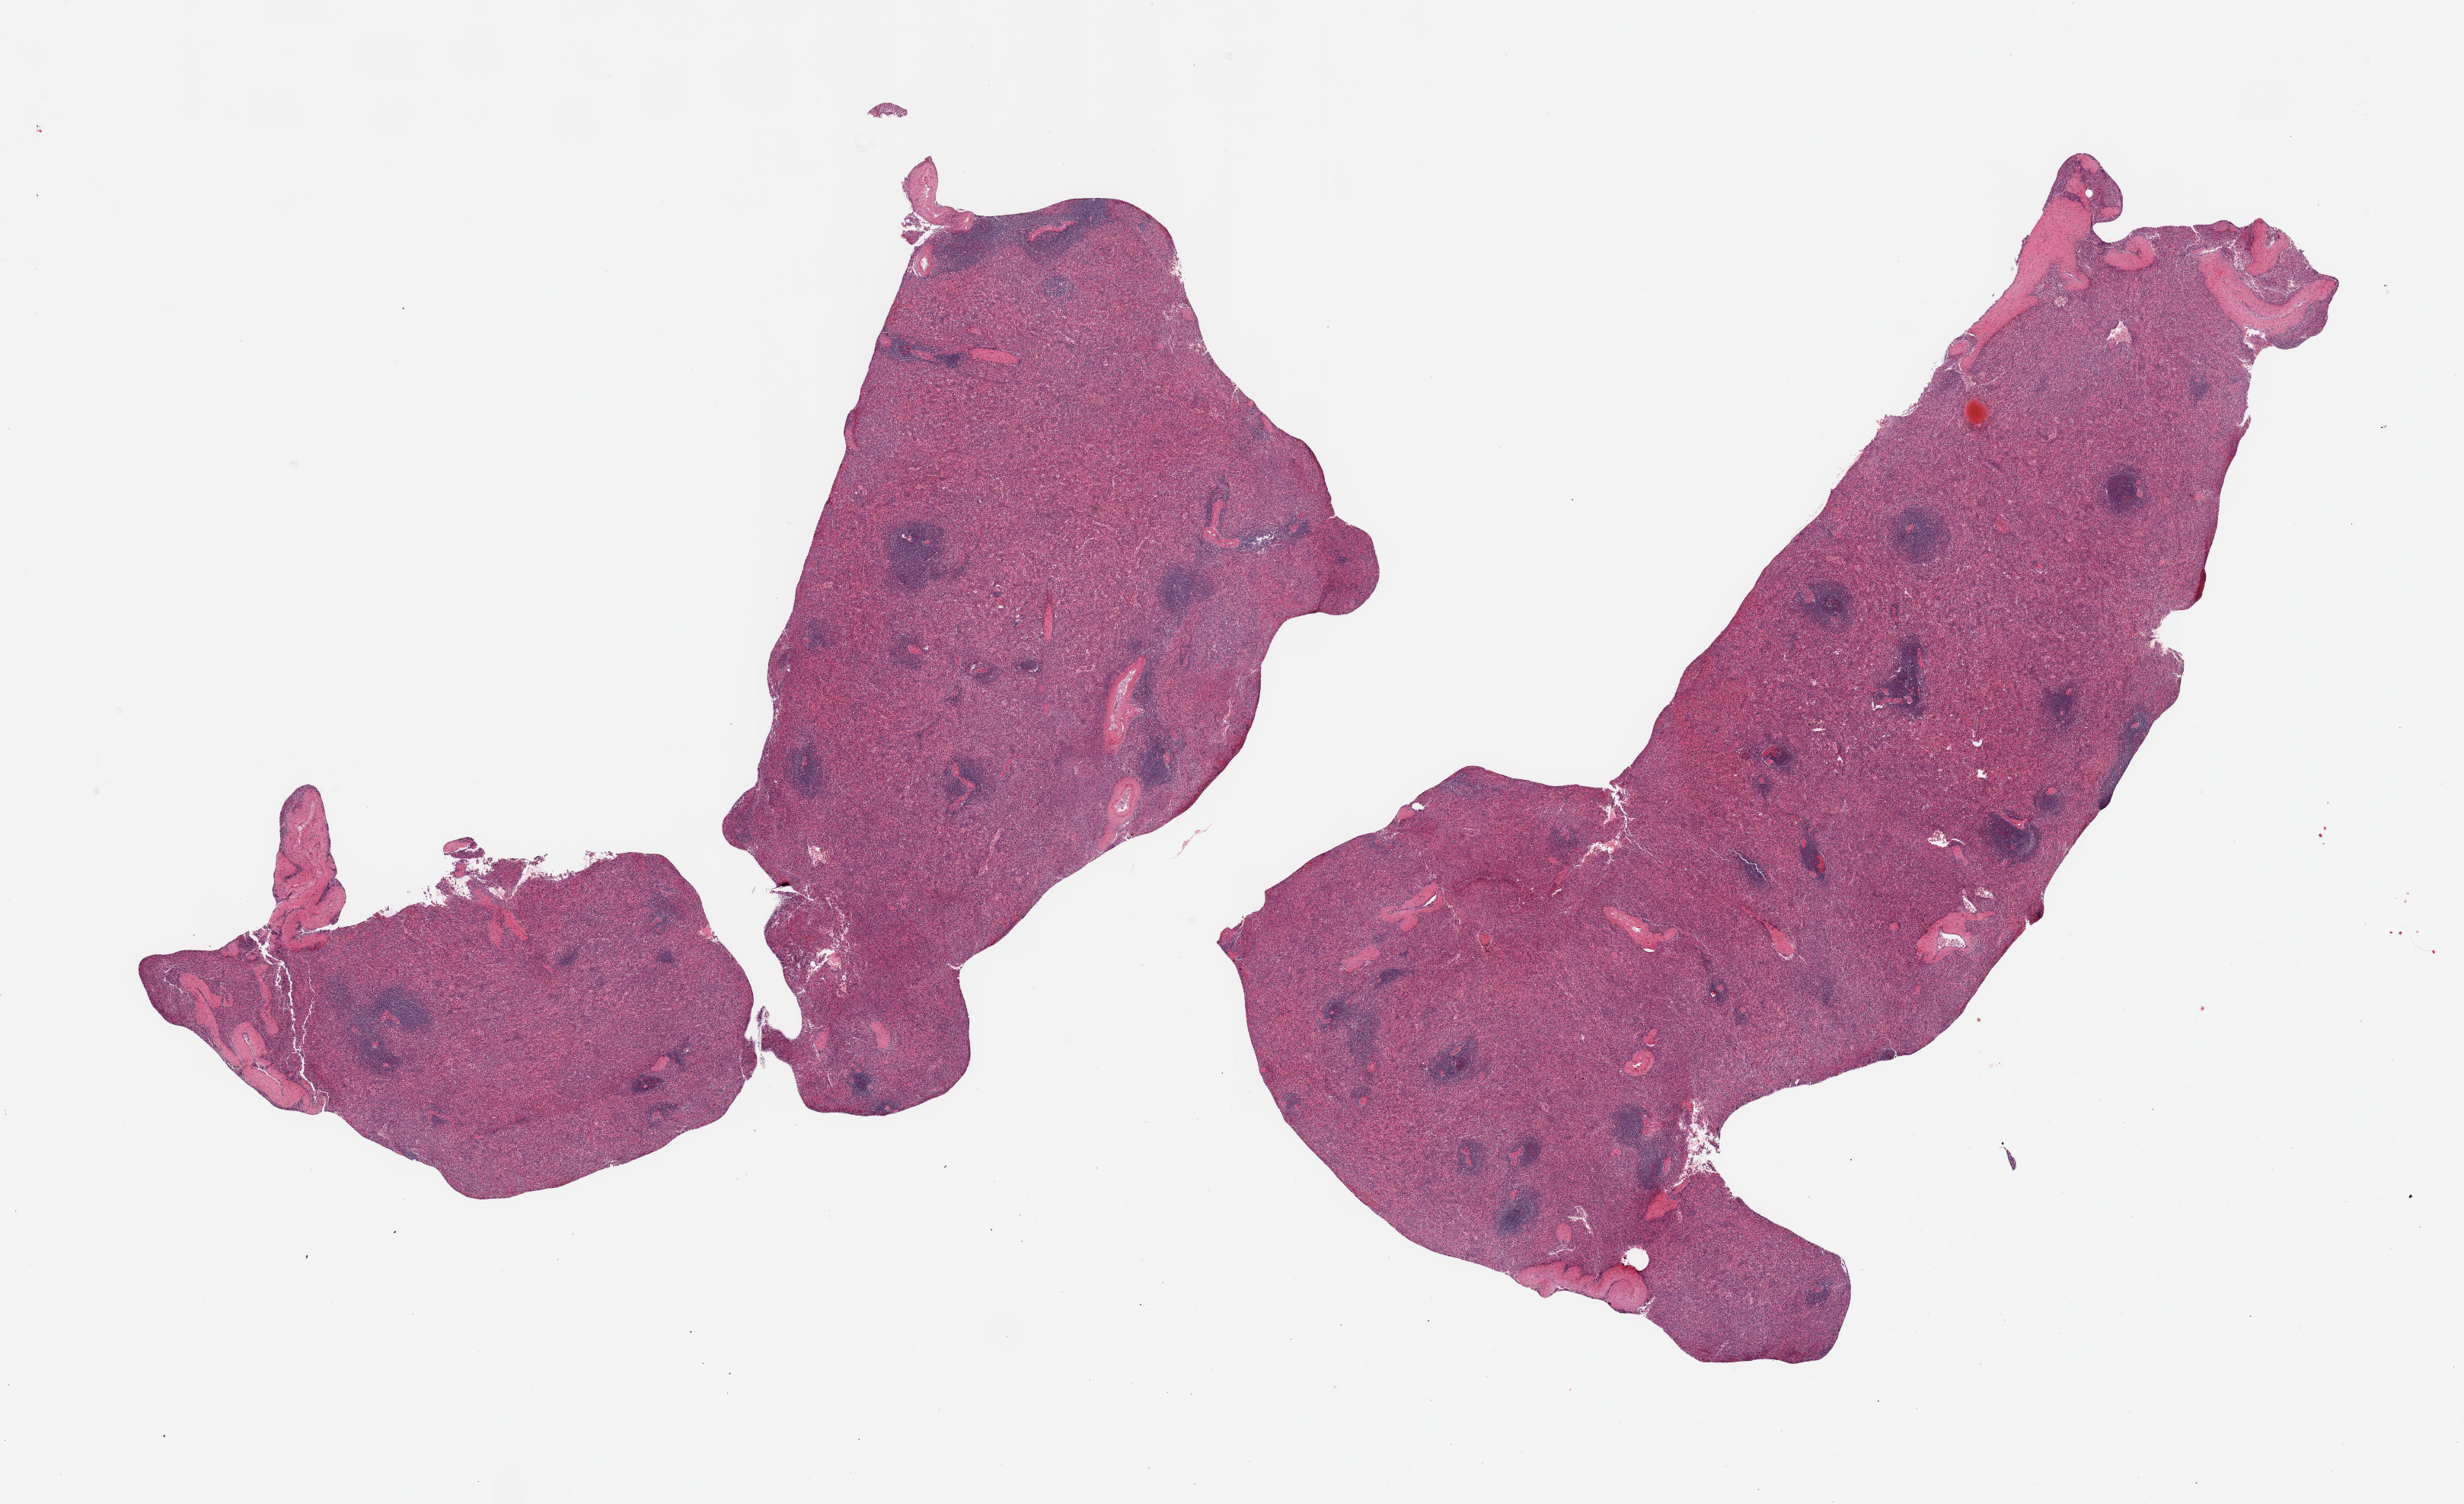
Hematoxylin and eosin (H&E) whole-slide image — low-resolution overview of the scanned area, about 25.6 x 15.6 mm, PAXgene-fixed paraffin-embedded (PFPE) section, sampled site (target tissue): spleen, tissue donor sample. Male donor.
Pathologist's review note for this sample: 2 pieces, moderate congestion.